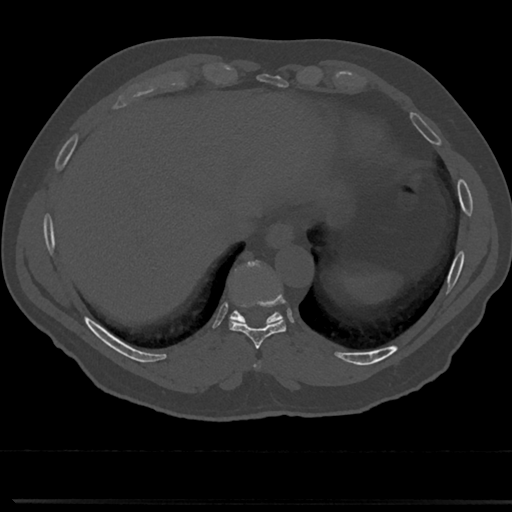
CT including the spine, one axial slice. Position 291 of 817 along the scan axis. Reconstruction kernel Br40s/3. 120 kVp. Bone window (W 1800 / L 400 HU). 512 × 512 image matrix, field of view 355 × 355 mm. Male patient, age 61 years. Case-level facts recorded for this patient, not image findings: primary cancer: prostate.
Structures marked on this image (semi-automatic segmentation, software-assisted and operator-edited):
- T8 vertebra: bounding box <254,339,266,363> (left, top, right, bottom; pixels)
- T9 vertebra: <214,265,301,349>